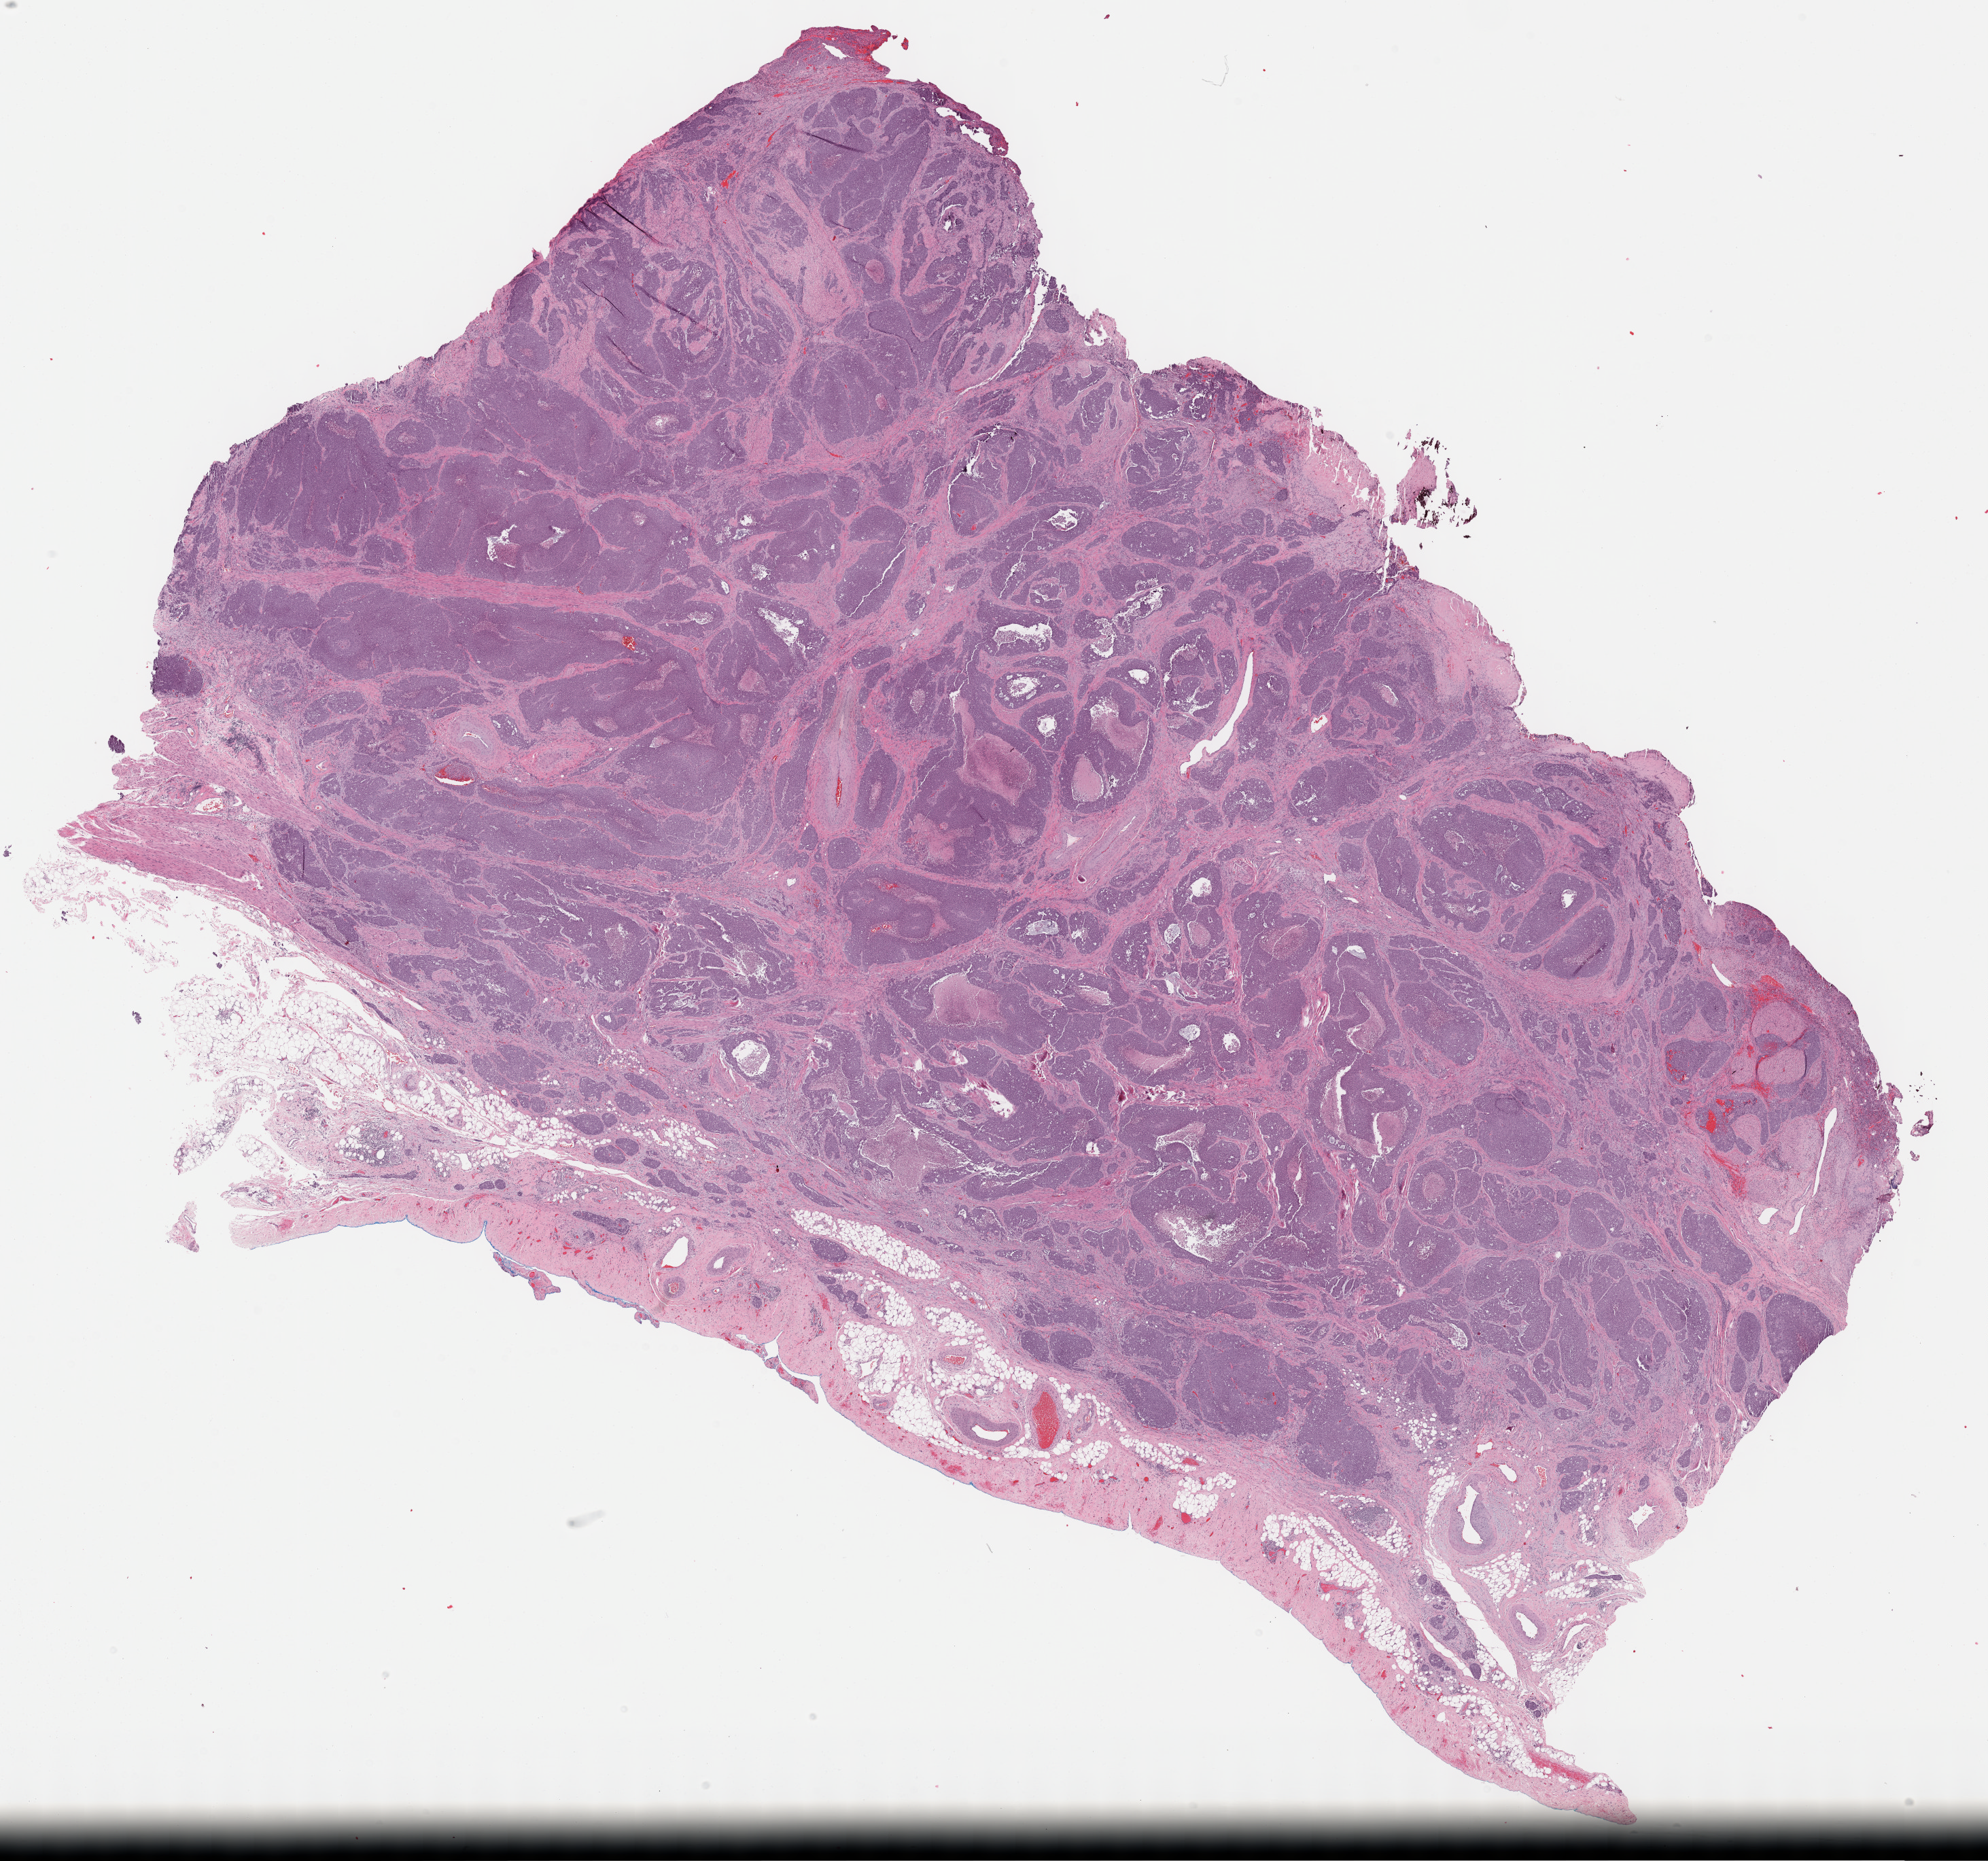
Digitized H&E-stained tissue section (whole slide) — shown as a low-resolution overview of the whole scanned area (about 23.7 x 22.1 mm); formalin-fixed paraffin-embedded (FFPE) diagnostic section; bladder, primary tumour sample. Male patient; age at initial diagnosis 84 years. Histologic grade: high grade.
• pathologic diagnosis: Transitional cell carcinoma
• lymph nodes positive (case pathology): 0 of 11 examined
• AJCC pathologic stage: III